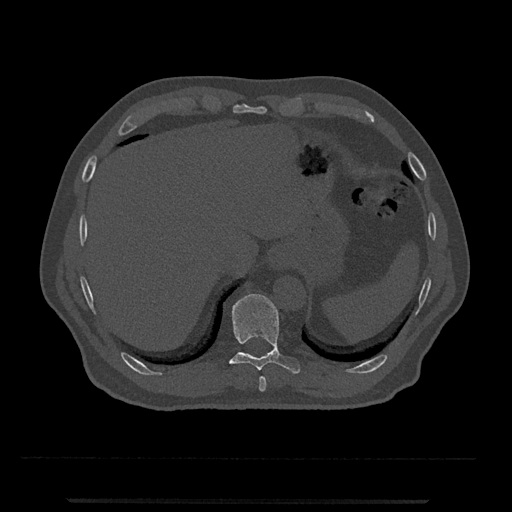
CT including the spine, one axial slice; bone window (W 1800 / L 400 HU); 512 × 512 image matrix, field of view 419 × 419 mm. Male patient, age 63 years. Case-level facts recorded for this patient, not image findings: primary cancer: prostate.
Outlined on this slice (semi-automatic segmentation, software-assisted and operator-edited):
- T10 vertebra: bounding box <229,294,301,374> (left, top, right, bottom; pixels)
- T9 vertebra: <259,376,267,392>